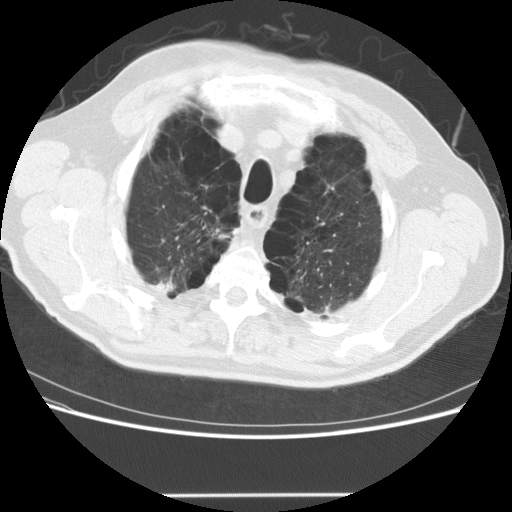
Chest CT (low-dose screening protocol), one axial image, third annual screen, lung window (W 1500 / L -600 HU), 2.5 mm slice thickness, standard (soft-tissue) reconstruction kernel (STANDARD), 512 × 512 image matrix, field of view 360 × 360 mm. Male participant, aged 68 years at enrolment. Former smoker at enrolment.
• Expert reader's lesion annotation, box from (x=125, y=218) to (x=213, y=304) px.
• The screening reader recorded 2 non-calcified nodules or masses ≥4 mm on this exam (lingula, left lower lobe); which of them this box marks is not recorded.
• Official screen result: positive, no significant change: stable abnormalities potentially related to lung cancer, unchanged since the prior screening exam.
• Participant outcome: lung cancer diagnosed 301 days after this screen — large cell carcinoma, NOS, right upper lobe, poorly differentiated (G3), stage IV (AJCC 6th edition).